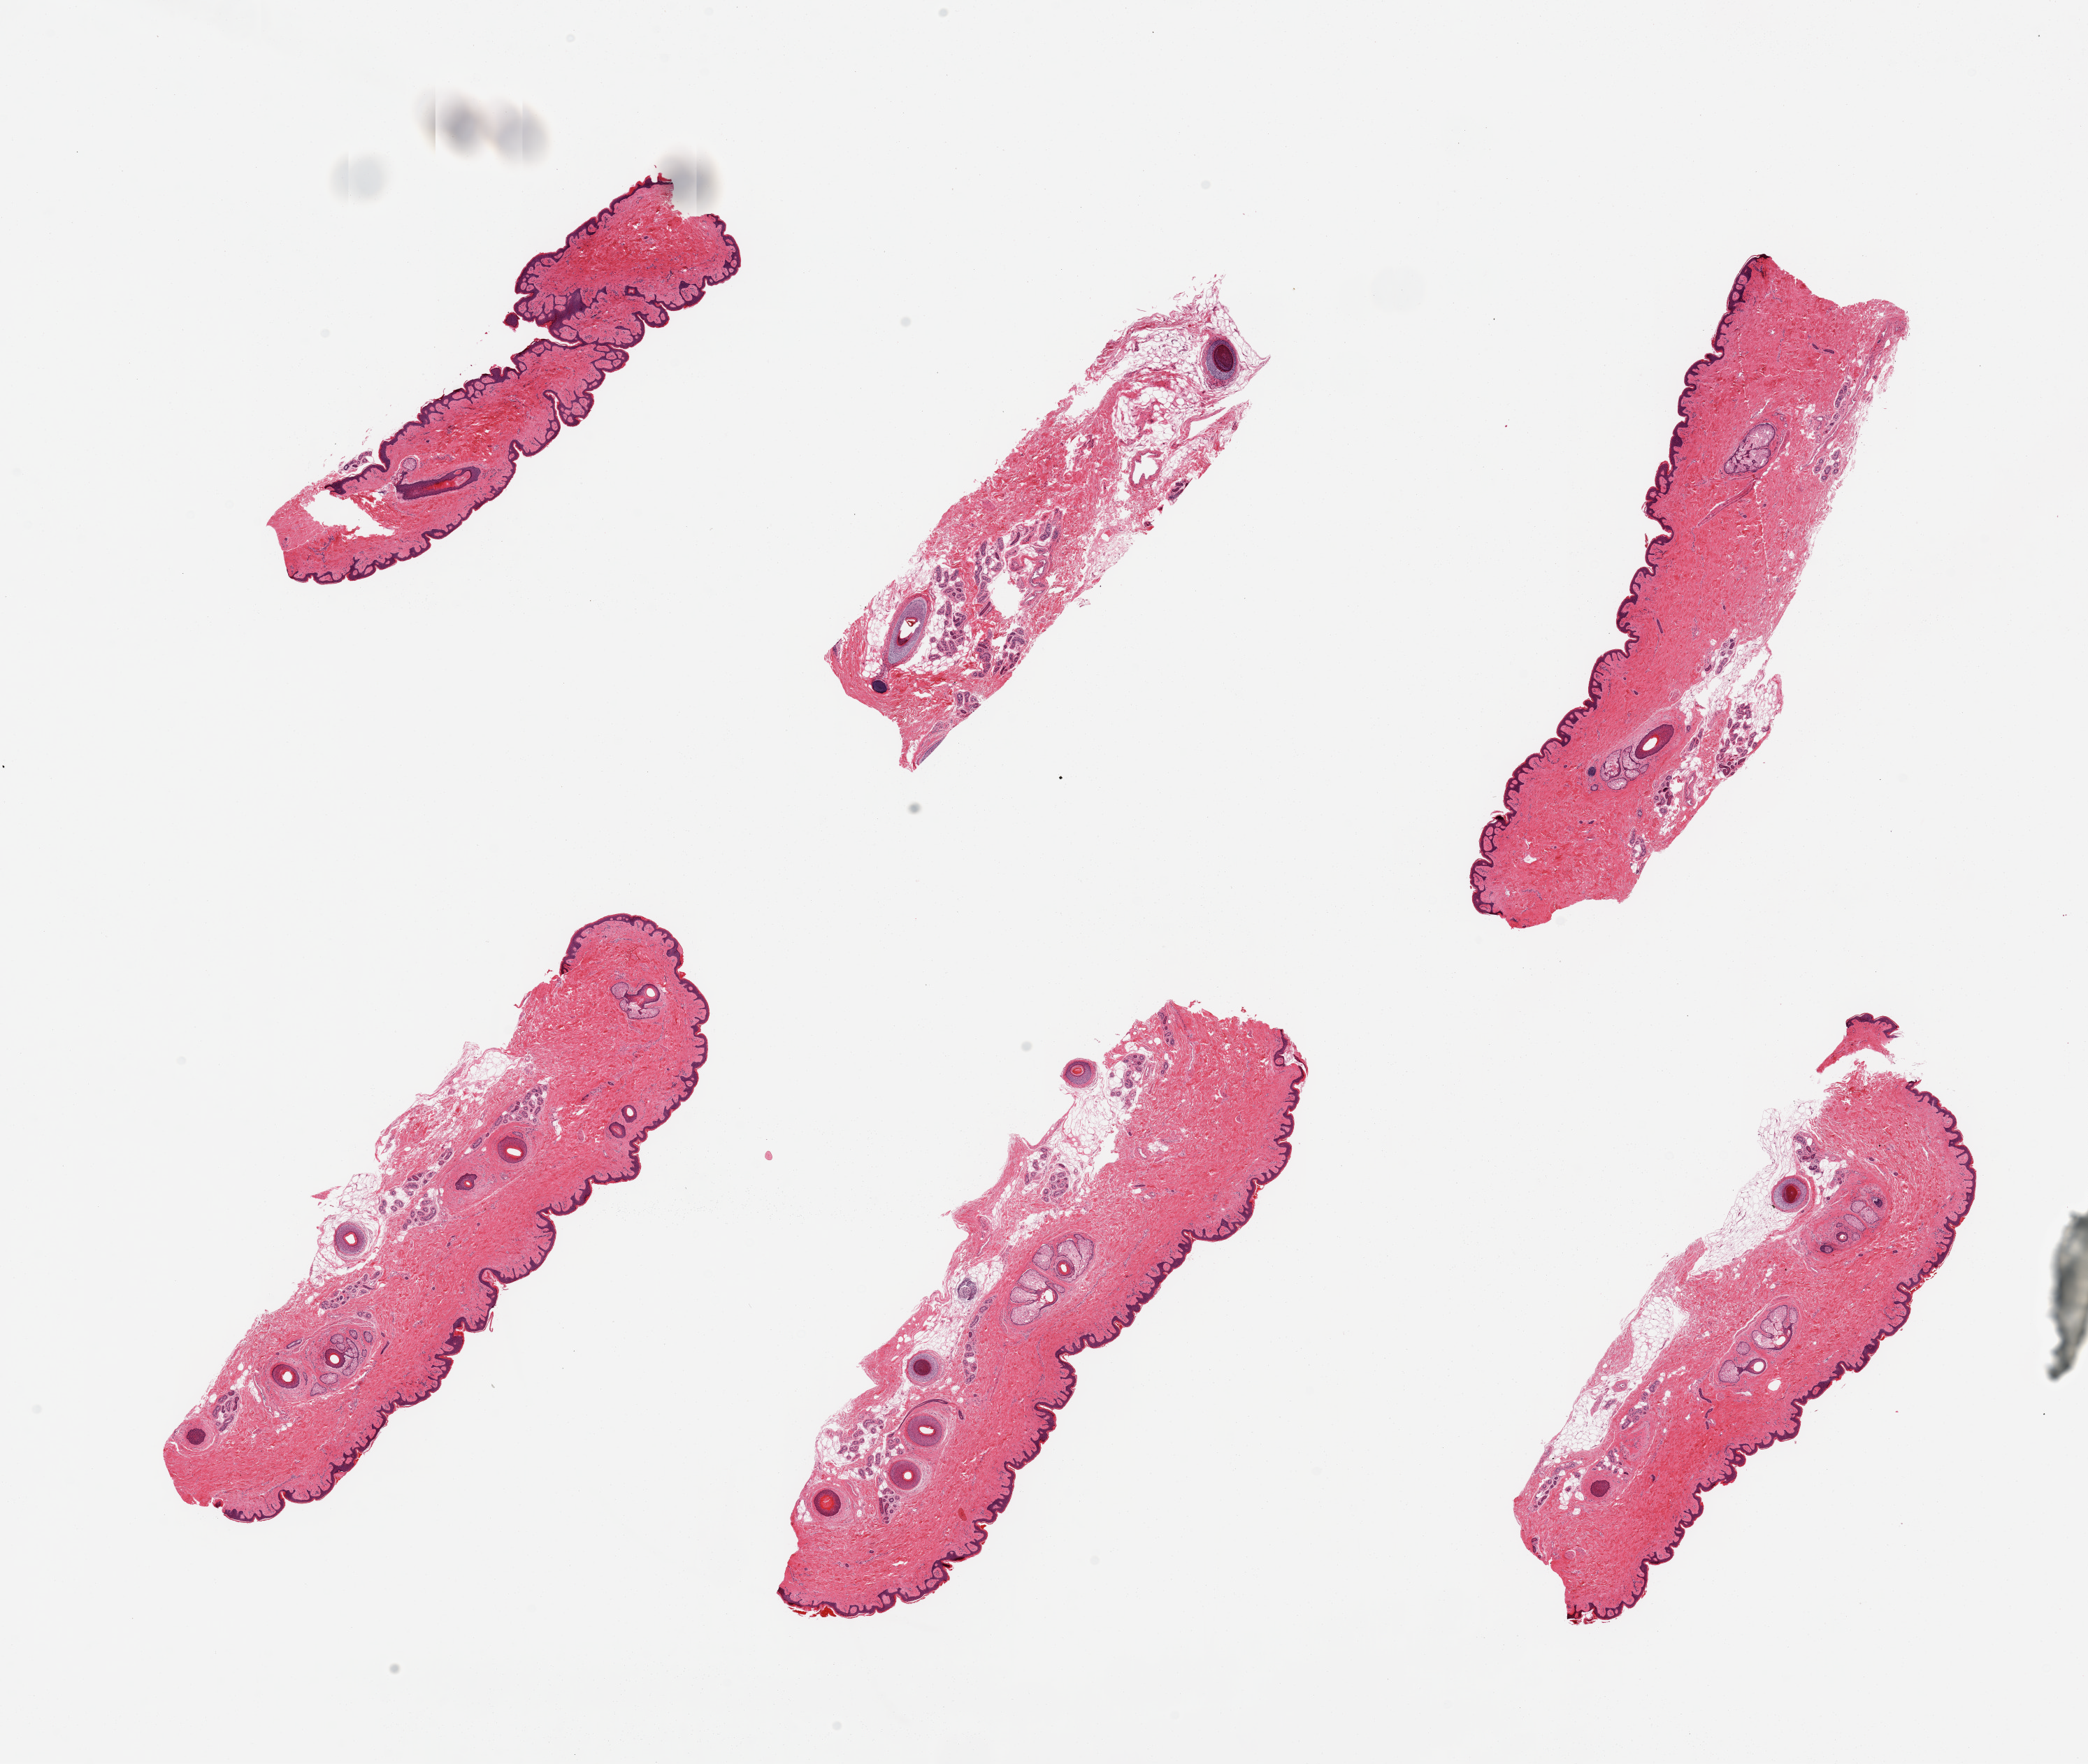
Digitized H&E-stained section, brightfield — a low-resolution overview of the entire scanned area, about 23.6 x 20.0 mm (from a 20x scan), PAXgene-fixed, paraffin-embedded tissue, sampled site (target tissue): skin of suprapubic region, donor tissue sample. Donor sex: male.
- pathologist's review note for this sample: 6 pieces, trace dermal fat; squamous epithelium is ~60microns. One section mis-embedded (squamous epithelium not visible)